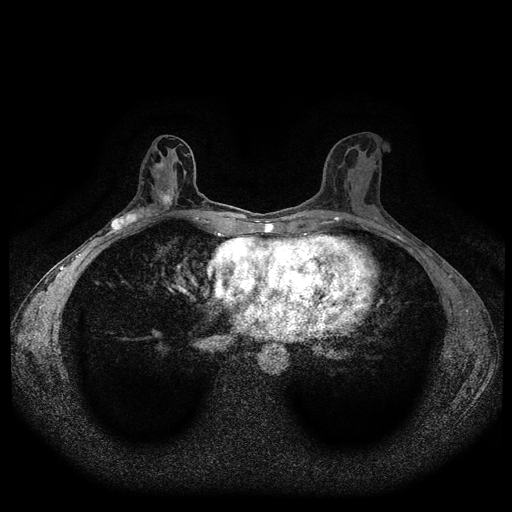
Breast MRI (dynamic contrast-enhanced, multi-phase), one axial slice. Slice 51 of 116 in the series (ordered by position). Dynamic contrast-enhanced series, time point 2 of 5 at this slice position (early post-contrast). 1.5 T. TE 2.6 ms, TR 5.3 ms. 2 mm slice thickness. 512 × 512 image matrix, field of view 350 × 350 mm. Female patient, age 50 years.
Outlined on this slice (semi-automatic segmentation, software-assisted and operator-edited):
- breast lesion (labelled 'tumour' in the annotation; benign lesions carry a separate 'benign' label): bounding box [x1, y1, x2, y2] px = [108, 186, 176, 233]